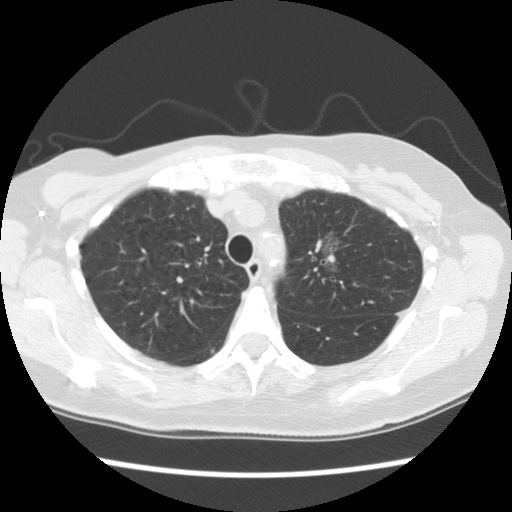
Axial slice from a low-dose chest CT screening exam, second screening round (one year after baseline), lung window (W 1500 / L -600 HU), standard (soft-tissue) reconstruction kernel (STANDARD), slice 81 of 110 in the series, 512 × 512 image matrix. Female participant, aged 65 years at enrolment.
• Lesion marked by an expert reader, bounding box (x1, y1, x2, y2) in pixels: (302, 223, 363, 285).
• The screening reader recorded 2 non-calcified nodules or masses ≥4 mm on this exam (right upper lobe, left upper lobe); which of them this box marks is not recorded.
• Later outcome: lung cancer diagnosed 481 days after this screen — adenocarcinoma, NOS, left upper lobe, moderately differentiated (G2), stage IA (AJCC 6th edition), 30 mm at pathology.